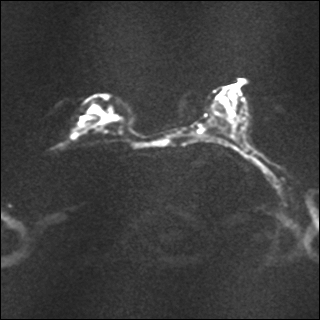
Breast MRI, one axial slice; position 17 of 35 along the scan axis; diffusion-weighted series; image 2 of 4 stored at this slice position (different b-values; order by instance number); 1.5 T; 4 mm slice thickness; 320 × 320 image matrix, field of view 317 × 317 mm. Female patient.
Structures marked on this image (manually delineated by an expert):
- tumour on diffusion-weighted imaging: box from (x=80, y=108) to (x=96, y=126) px